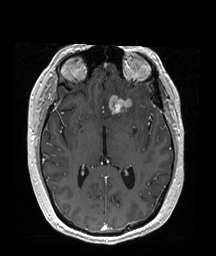
Brain MRI from a brain-tumour surgery series, one axial slice. Position 100 of 192 along the scan axis. T1-weighted post-contrast. 1 mm slice thickness. 216 × 256 image matrix, field of view 211 × 250 mm. From the clinical record (not read from this slice): histopathology: Oligodendroglioma; WHO grade: 2; IDH mutation: yes; tumour location: Left Frontal (septal).
Structures marked on this image (outlined manually by an expert reader):
- tumour: bounding box [x1, y1, x2, y2] px = [107, 95, 132, 117]